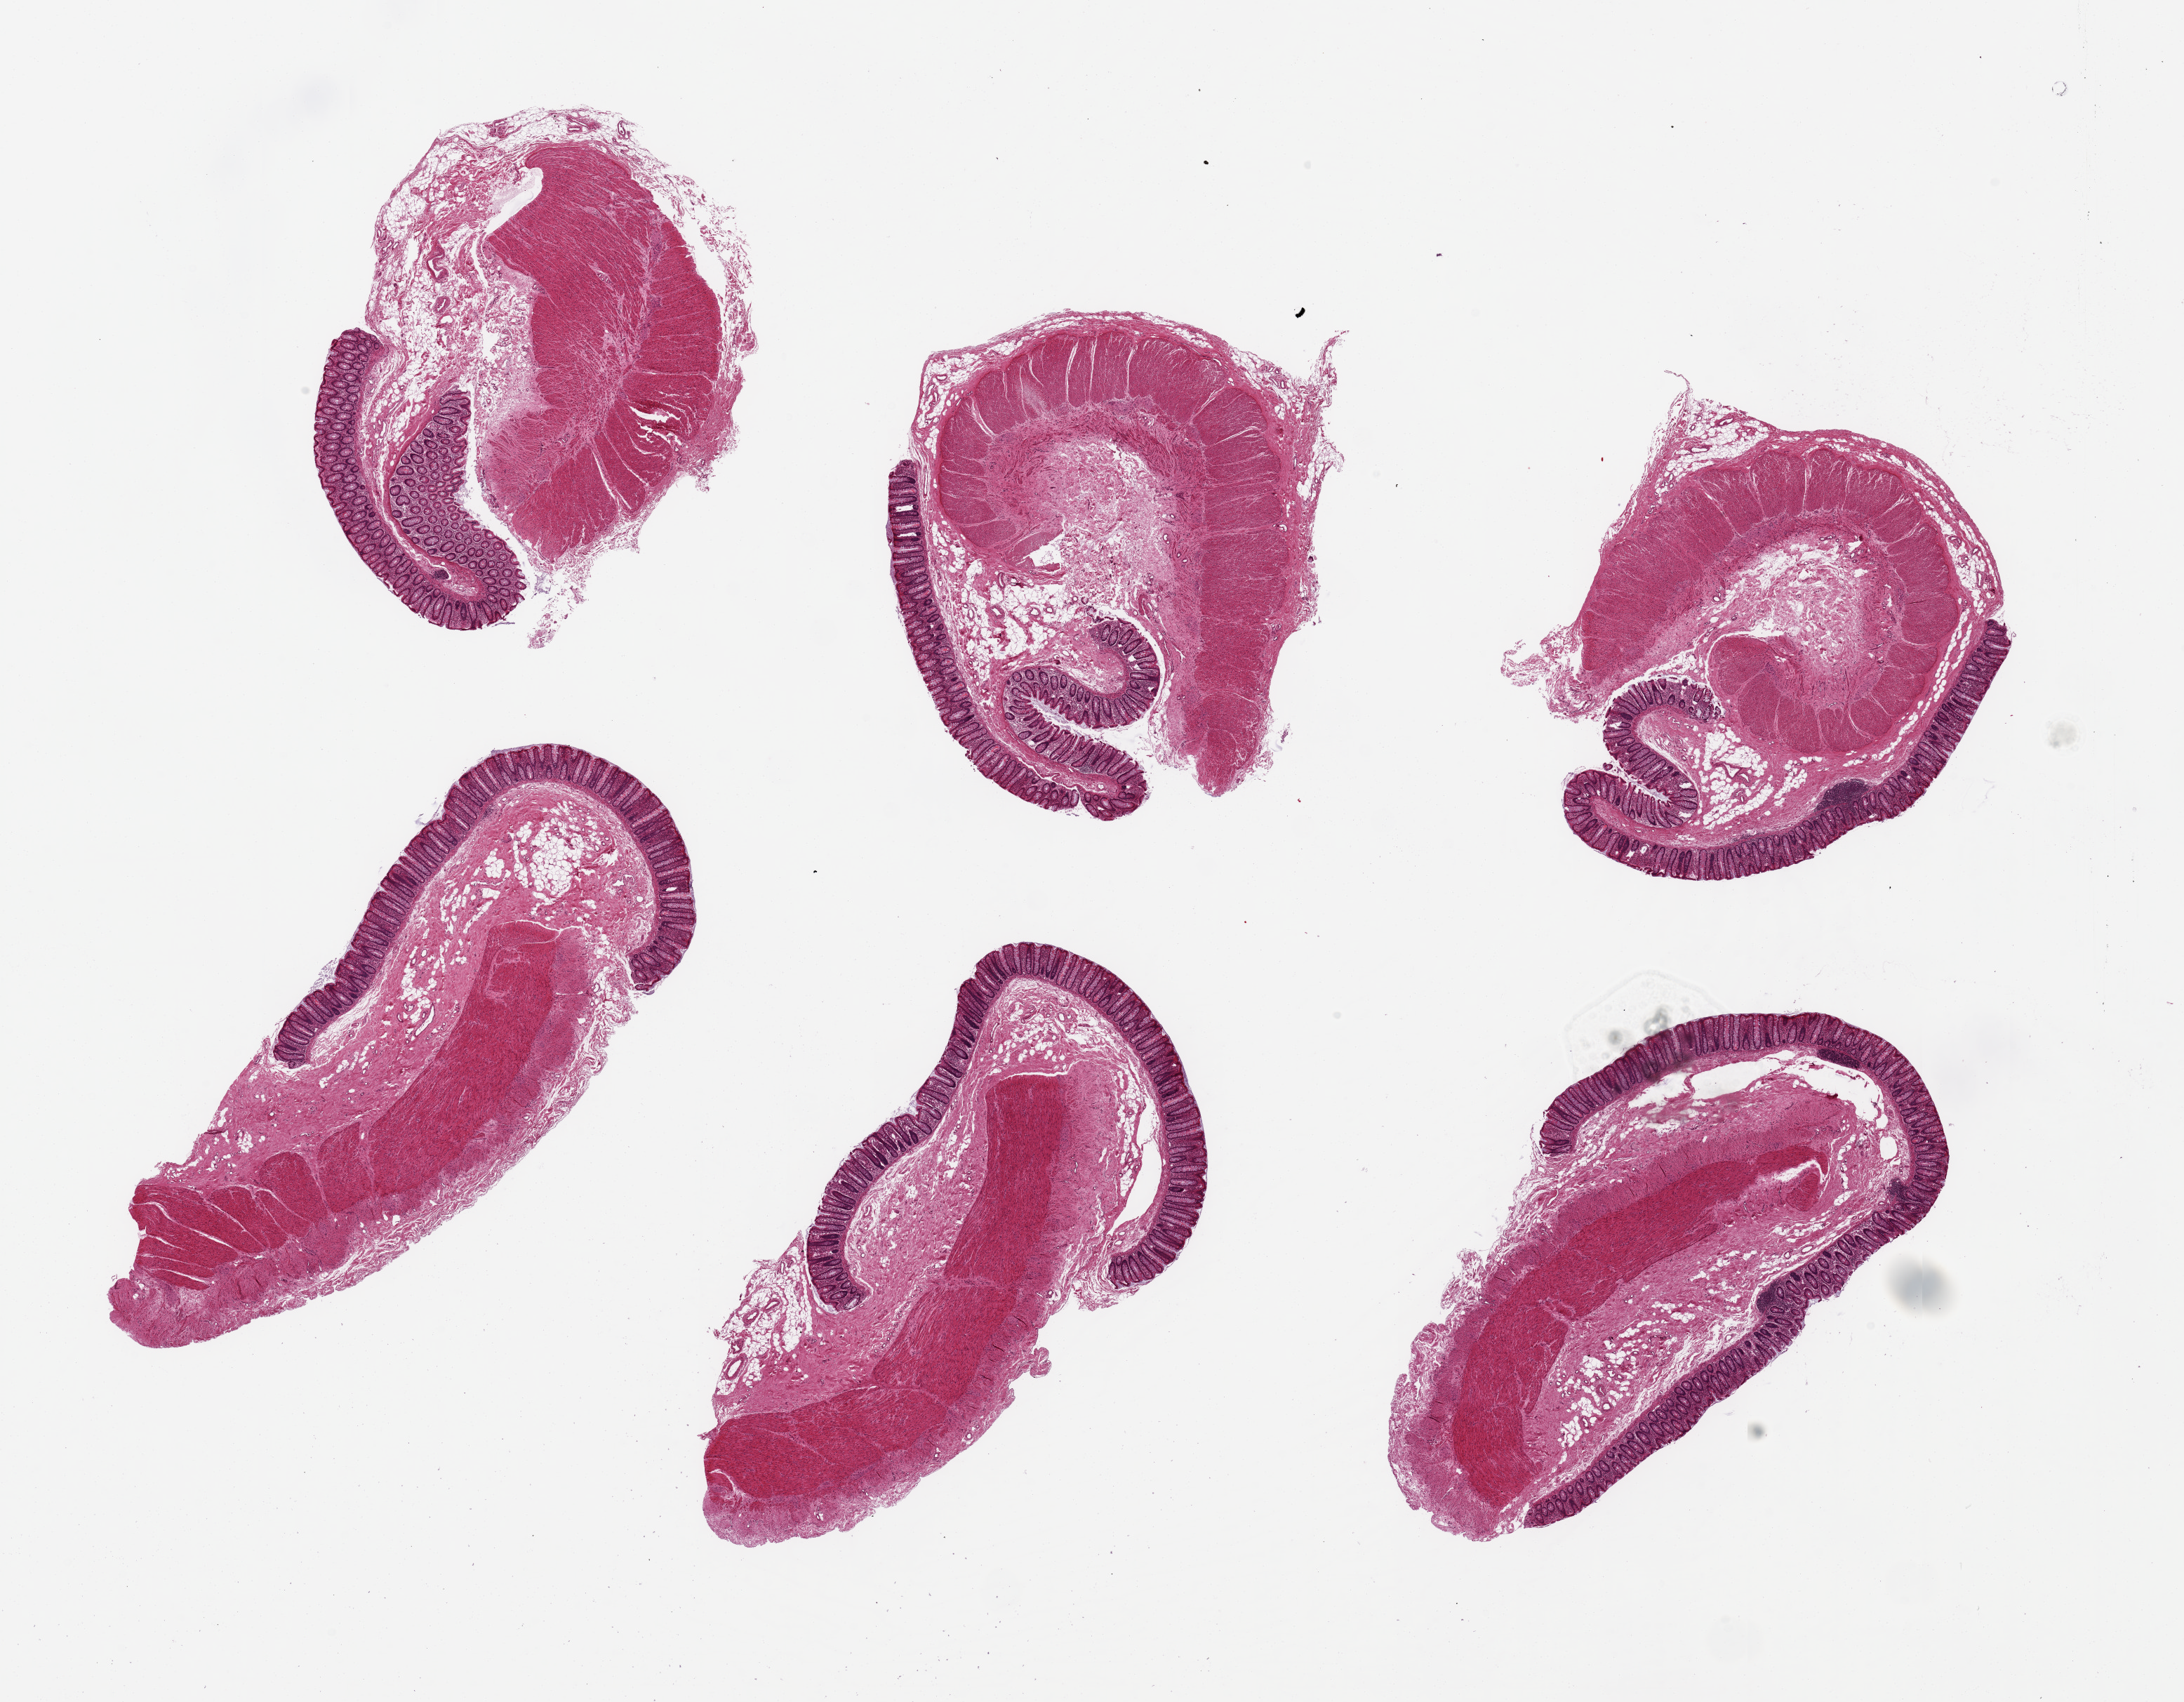
H&E whole-slide image, brightfield, shown as a low-resolution overview of the whole scanned area (about 24.6 x 19.2 mm), PAXgene-fixed, paraffin-embedded tissue, section of transverse colon (target tissue), donor tissue sample.
• reviewer comment on this tissue sample: 6 pieces up to 8x3 mm; good mucosal preservation